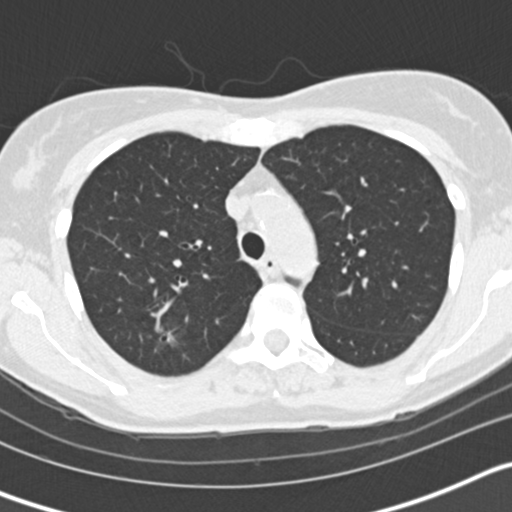
Low-dose screening chest CT, one axial slice. Slice 117 of 163 in the series (ordered by position). Reconstruction kernel B30f. 120 kVp. Lung window (W 1500 / L -600 HU). 2 mm slice thickness. 512 × 512 image matrix, field of view 300 × 300 mm.
Outlined on this slice (outlined manually by an expert reader):
- lesion 1 (tumor, upper lobe of right lung): box from (x=167, y=331) to (x=174, y=343) px